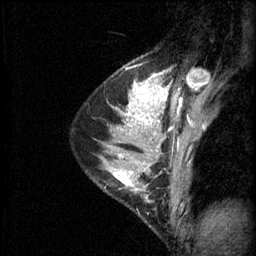
Breast MRI (dynamic contrast-enhanced), one sagittal slice; slice 39 of 60 in the series (ordered by position); 3 images stored at this slice position (order not interpretable as contrast timing); 1.5 T; TE 4.2 ms, TR 11 ms; 2.1 mm slice thickness; 256 × 256 image matrix, field of view 180 × 180 mm. Patient: female, 29 years.
Annotated regions visible in this slice (semi-automatically segmented with operator editing):
- analysis volume of interest (the breast-tissue region the enhancement analysis was run in; not a lesion): bounding box (x1, y1, x2, y2) in pixels: (104, 164, 153, 201)
- tumour enhancement mask (voxels above the 70 % enhancement threshold inside the analysis volume of interest): (109, 170, 145, 189)